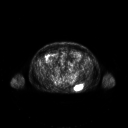
FDG PET of an extremity soft-tissue mass (from a PET/CT study), one axial slice. Position 83 of 267 along the scan axis. 3.27 mm slice thickness. 128 × 128 image matrix. Male patient, age 61 years. From the clinical record (not read from this slice): histological type: pleiomorphic leiomyosarcoma; grade: high; site of the primary tumour: left buttock.
Annotated regions visible in this slice (expert contour drawn on MRI and transferred to this co-registered scan by the dataset authors):
- gross tumour volume including surrounding oedema: bounding box <74,84,84,91> (left, top, right, bottom; pixels)
- gross tumour volume (mass): <75,85,83,90>